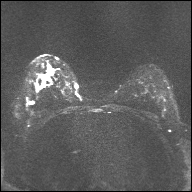
Breast MRI, one axial slice; position 22 of 32 along the scan axis; diffusion-weighted series; image 2 of 4 stored at this slice position (different b-values; order by instance number); 1.5 T; 4 mm slice thickness; 192 × 192 image matrix. Female patient.
Annotated regions visible in this slice (outlined manually by an expert reader):
- tumour on diffusion-weighted imaging: bounding box (x1, y1, x2, y2) in pixels: (44, 76, 50, 80)